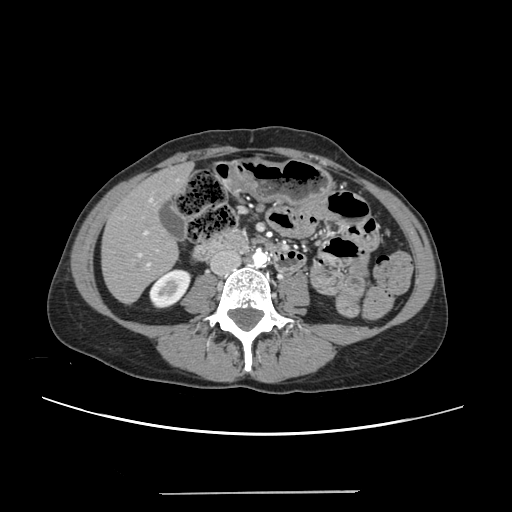
Contrast-enhanced abdominal CT, one axial slice. Slice 69 of 240 in the series (ordered by position). 120 kVp. Intravenous contrast given. Soft-tissue window (W 400 / L 40 HU). 1.25 mm slice thickness. 512 × 512 image matrix, field of view 371 × 371 mm. Female patient, age 60 years. From the clinical record (not read from this slice): diagnosis: colorectal cancer liver metastases, imaged before liver resection; multiple liver metastases: no; largest metastasis: 1.5 cm; chemotherapy before resection: yes.
Structures marked on this image (outlined manually by an expert reader):
- liver: bounding box [x1, y1, x2, y2] px = [103, 166, 188, 301]
- planned liver remnant (the part of the liver to remain after resection): [103, 171, 178, 302]
- portal vein (with intrahepatic branches): [138, 197, 158, 266]